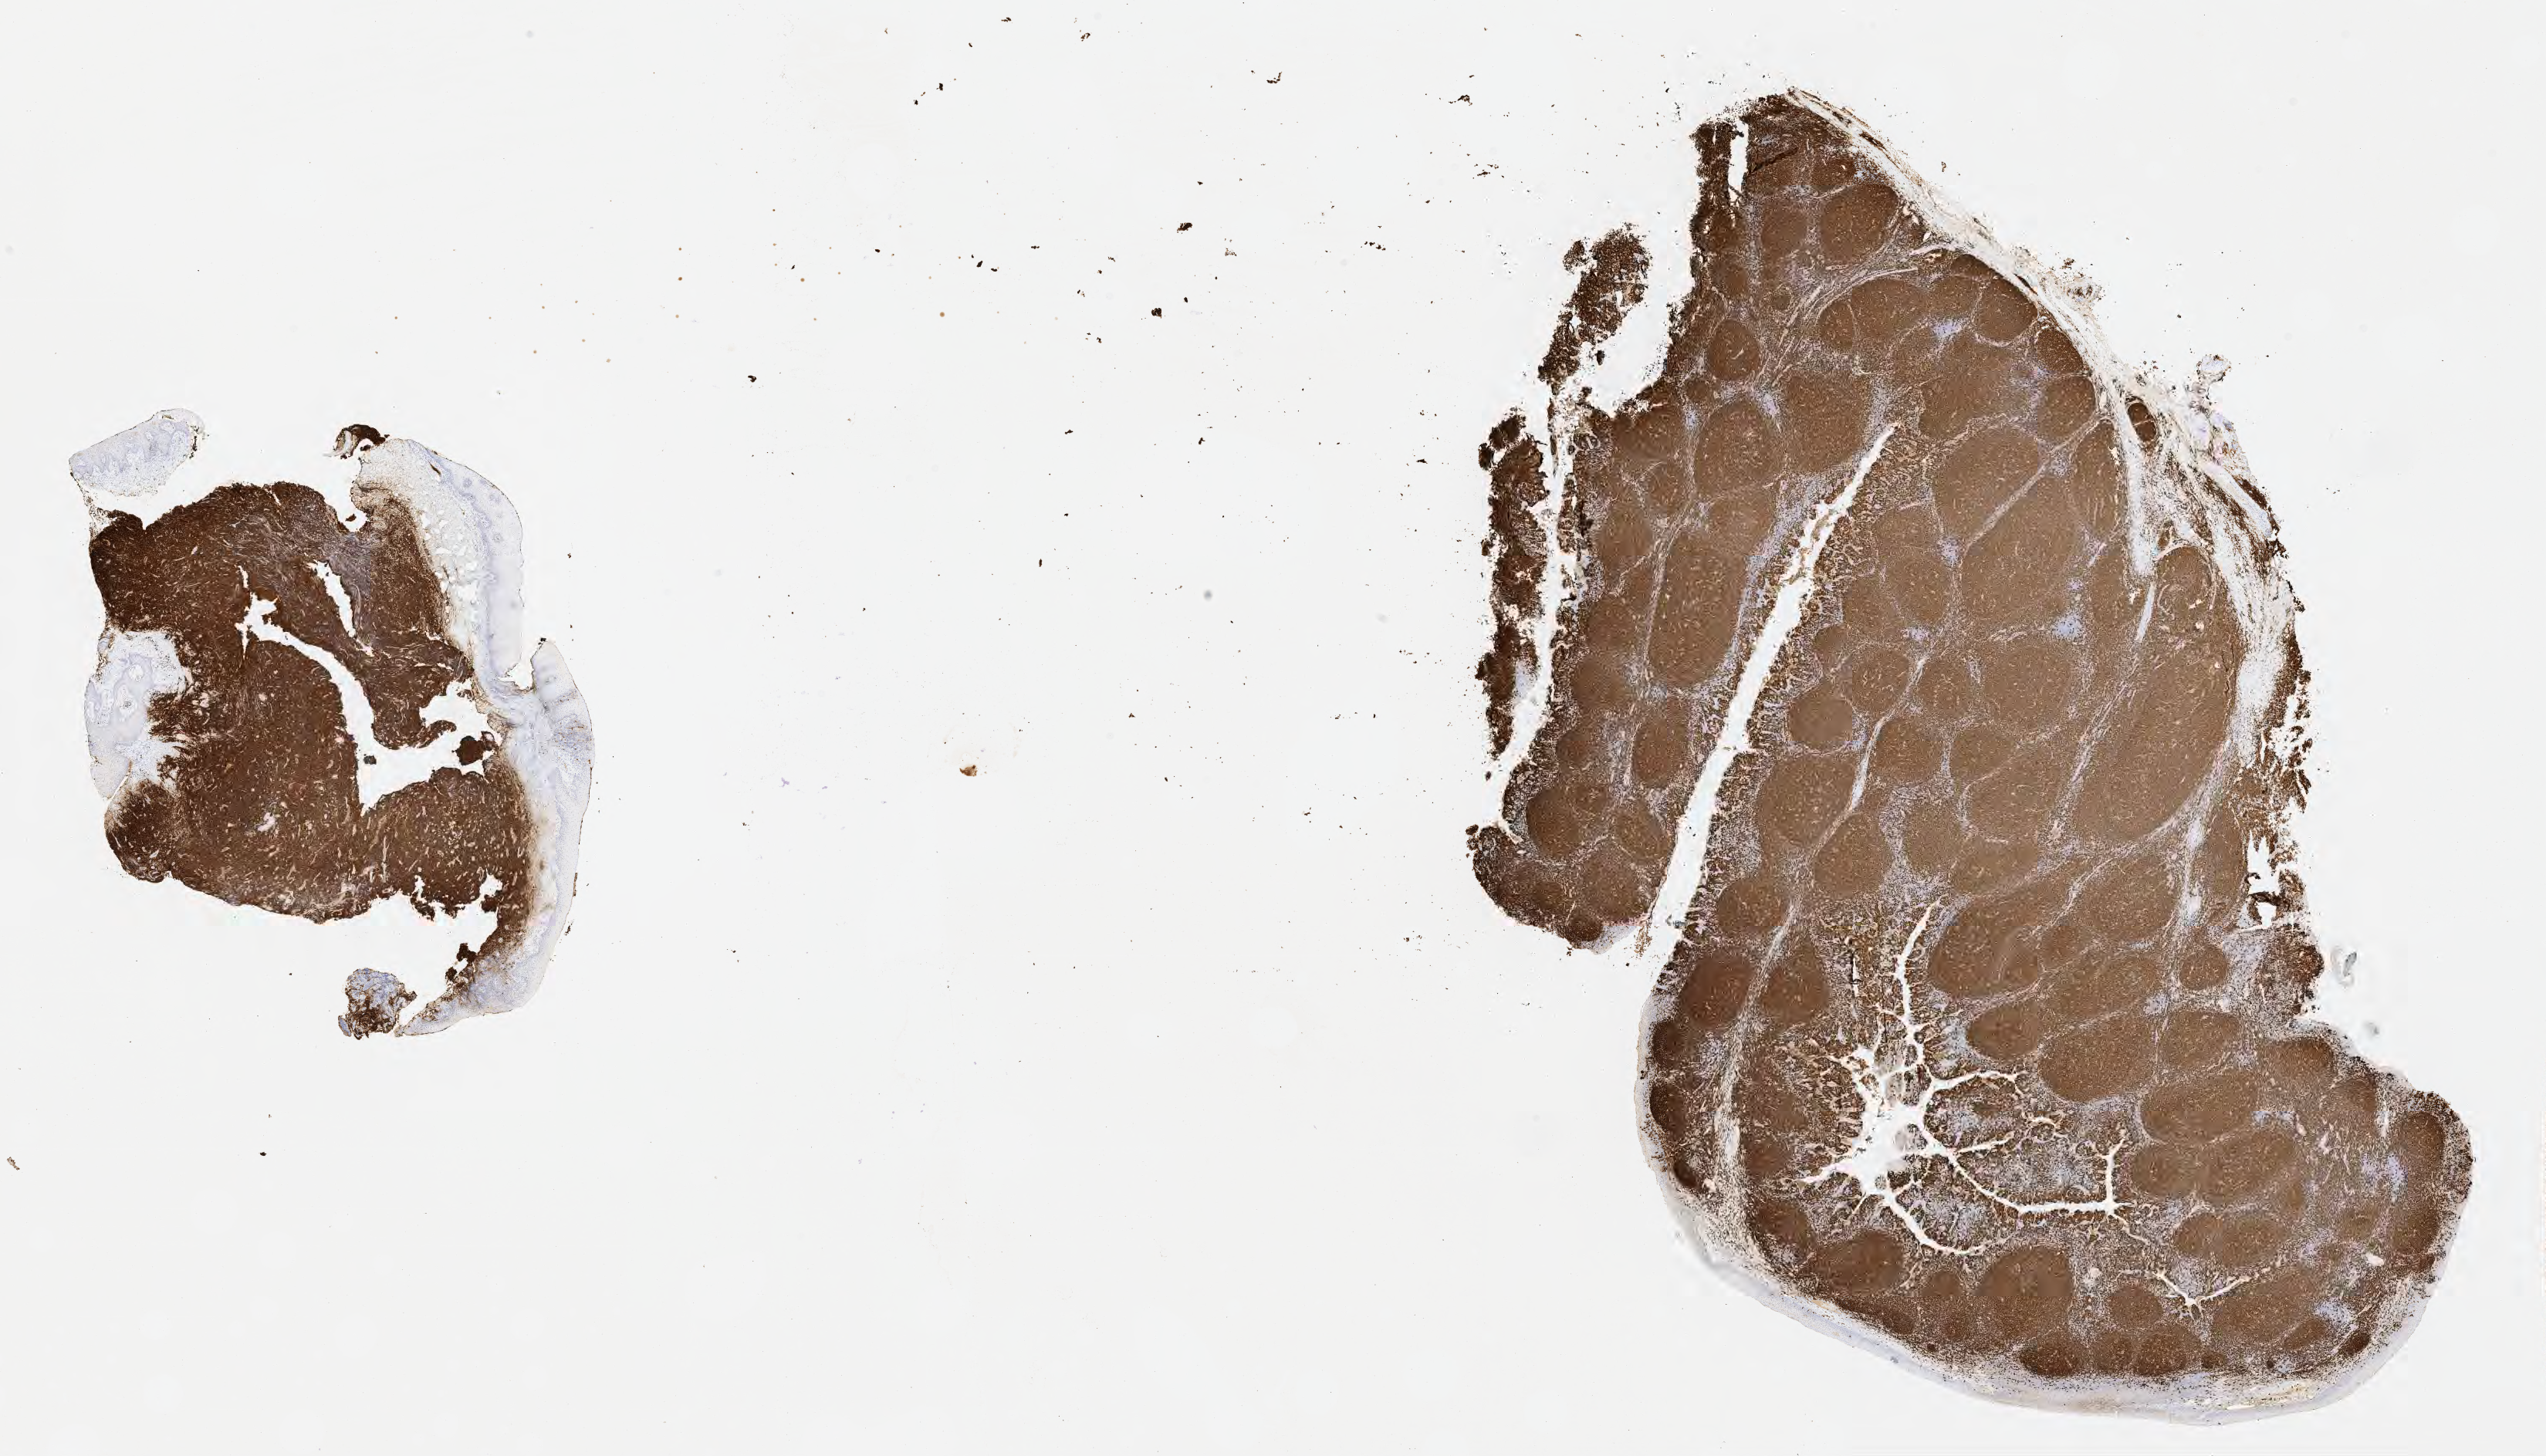
IHC for CD20, whole-slide image — a low-resolution overview of the entire scanned area, about 26.7 x 15.2 mm, tumor tissue, anatomic site: mandible. Female, age 7 years at initial diagnosis.
- diagnosis: Burkitt lymphoma, NOS